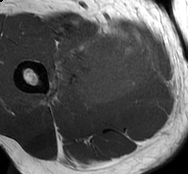
MRI of an extremity soft-tissue mass, one axial slice; slice 31 of 93 in the series (ordered by position); MR volume resampled by the dataset authors to the PET/CT grid (not the native acquisition matrix); 3.27 mm slice thickness; 188 × 174 image matrix, field of view 184 × 170 mm. Male patient. Case-level facts recorded for this patient, not image findings: histological type: undifferentiated - pleiomorphic; grade: high; site of the primary tumour: right thigh.
Structures marked on this image (expert contour drawn on MRI and transferred to this co-registered scan by the dataset authors):
- gross tumour volume including surrounding oedema: bounding box <47,24,158,105> (left, top, right, bottom; pixels)
- gross tumour volume (mass): <75,30,156,105>